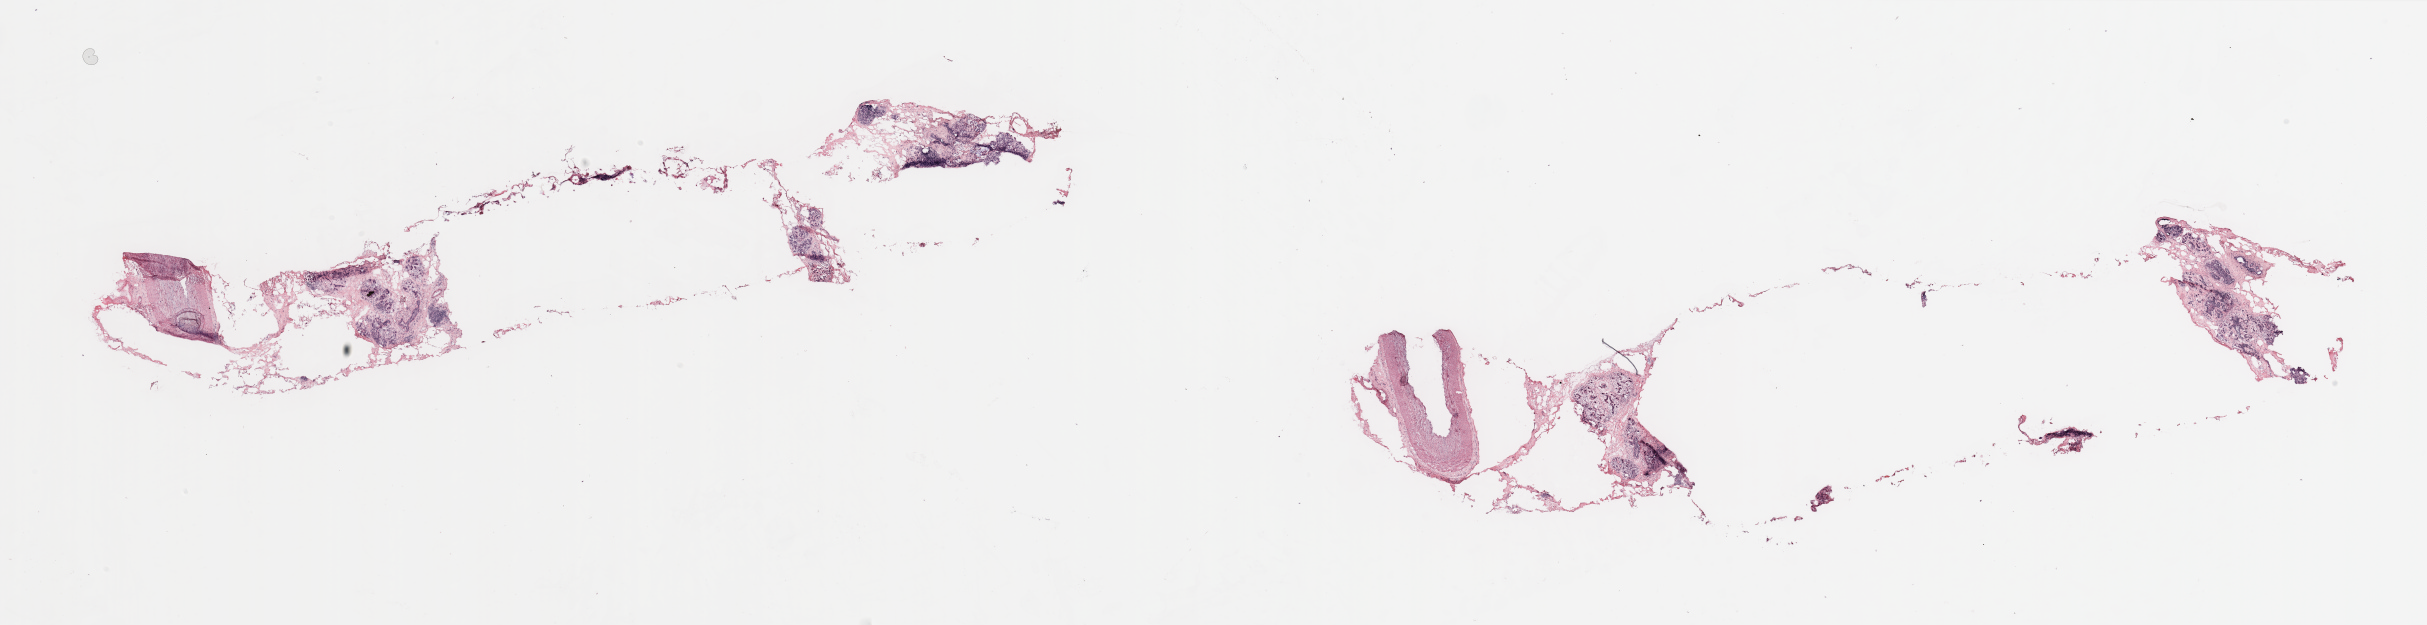
H&E whole-slide image — a low-resolution overview of the entire scanned area, about 38.4 x 9.9 mm. Female, 48 y/o.
- specimen: breast, tumour tissue